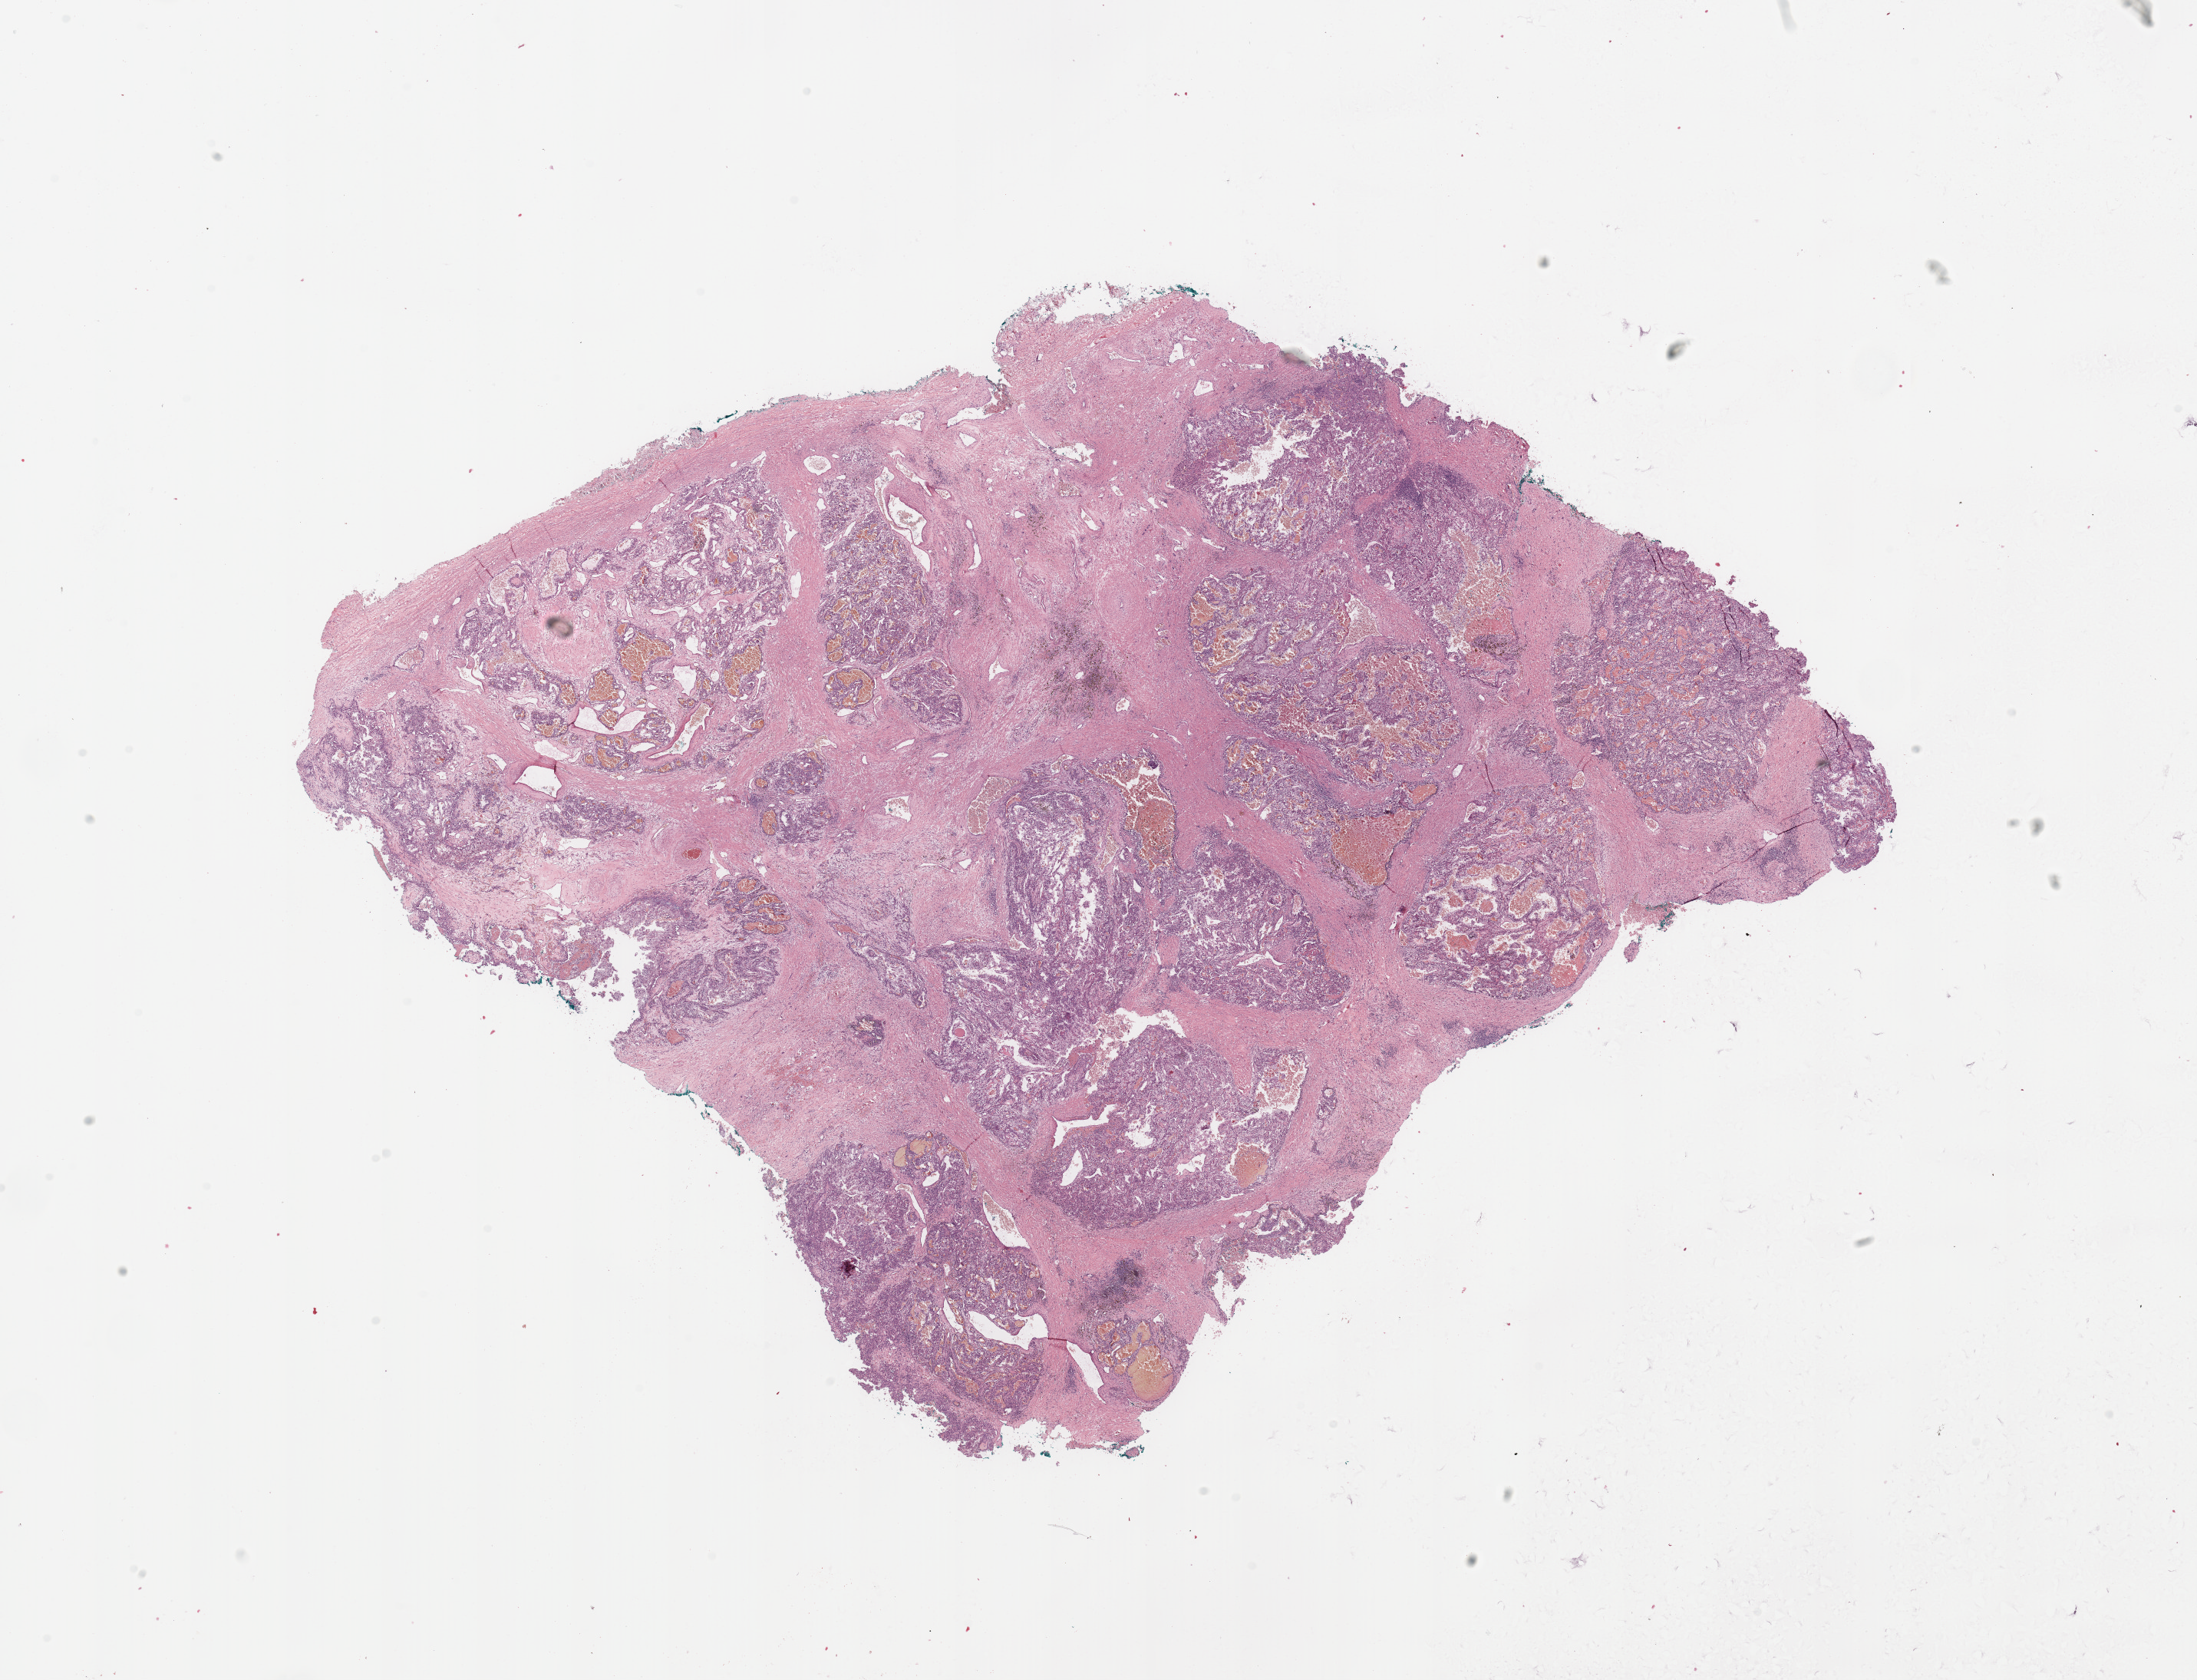
Digitized H&E-stained tissue section (whole slide), whole scanned area (about 22.6 x 17.3 mm) shown as a low-resolution overview, tumour tissue sample, kidney. Male, 45 y/o. Histologic grade: G2 (moderately differentiated).
Histologic diagnosis: Renal cell carcinoma, NOS. AJCC pathologic stage: II. Primary tumour site (as recorded): middle.